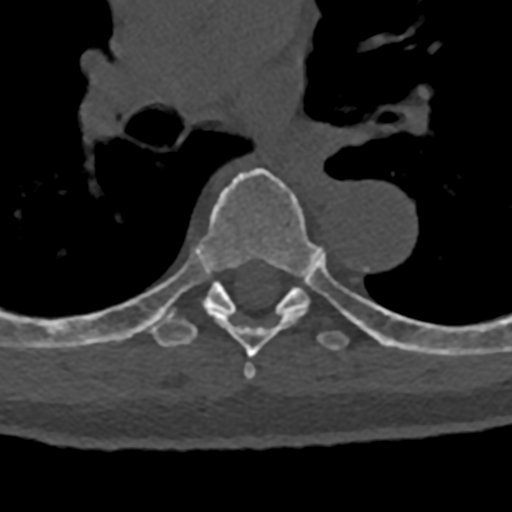
CT including the spine, one axial slice. Position 793 of 797 along the scan axis. Bone window (W 1800 / L 400 HU). 512 × 512 image matrix, field of view 160 × 160 mm. Male patient, age 74 years. Case-level facts recorded for this patient, not image findings: primary cancer: renal.
Annotated regions visible in this slice (semi-automatic segmentation, software-assisted and operator-edited):
- T6 vertebra: bounding box [x1, y1, x2, y2] px = [143, 168, 318, 380]
- T7 vertebra: [70, 246, 432, 355]